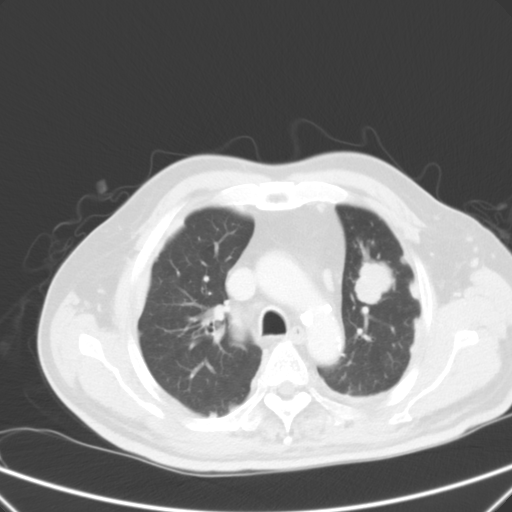
Chest CT, one axial slice. Slice 42 of 59 in the series (ordered by position). Intravenous contrast given. Lung window (W 1500 / L -600 HU). 5 mm slice thickness. 512 × 512 image matrix. Patient: male, 66 years. From the clinical record (not read from this slice): clinical TNM (as recorded): T1c N3 M1a.
Annotated regions visible in this slice (bounding box drawn by a radiologist):
- lung tumour (recorded histology: squamous cell carcinoma): bounding box (x1, y1, x2, y2) in pixels: (350, 251, 407, 308)